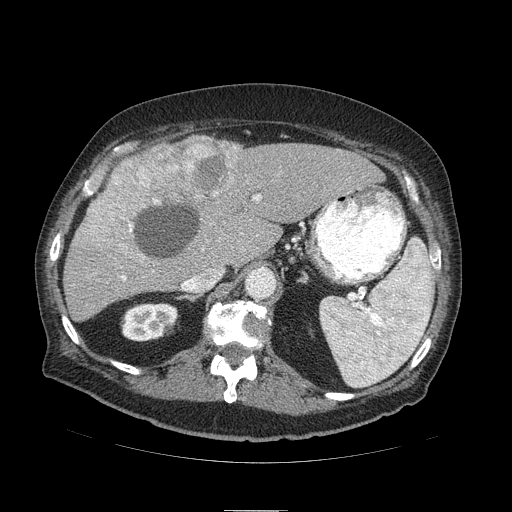
Contrast-enhanced abdominal CT (liver protocol), one axial slice. Slice 60 of 103 in the series (ordered by position). 120 kVp. Soft-tissue window (W 400 / L 40 HU). 2.5 mm slice thickness. 512 × 512 image matrix, field of view 440 × 440 mm. From the clinical record (not read from this slice): diagnosis: hepatocellular carcinoma (patient treated with transarterial chemoembolisation; whether this scan precedes or follows treatment is not stated here); TNM stage (as recorded): Stage-IIIA; Child-Pugh class: B; tumour size: 13 cm.
Annotated regions visible in this slice (semi-automatic segmentation, software-assisted and operator-edited):
- liver parenchyma outside the tumour (the mass and vessels are separate outlines, so this box may not span the whole liver): bounding box (x1, y1, x2, y2) in pixels: (62, 144, 384, 322)
- mass: (76, 135, 245, 251)
- liver vessels: (122, 195, 260, 280)